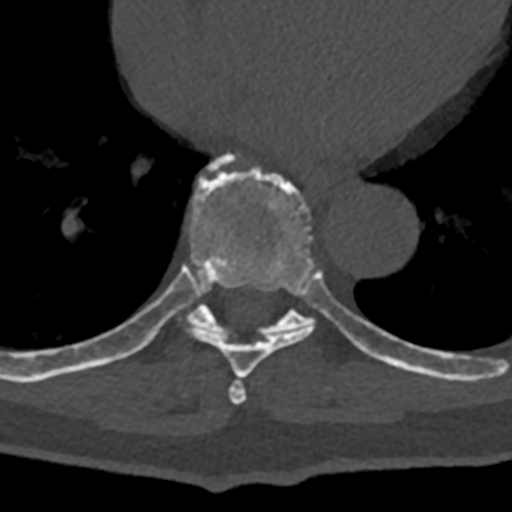
CT including the spine, one axial slice. Slice 690 of 797 in the series (ordered by position). 120 kVp. Bone window (W 1800 / L 400 HU). 512 × 512 image matrix. Patient: male, 74 years. Case-level facts recorded for this patient, not image findings: primary cancer: renal.
Structures marked on this image (semi-automatic segmentation, software-assisted and operator-edited):
- T7 vertebra: bounding box [x1, y1, x2, y2] px = [229, 377, 247, 404]
- T8 vertebra: [70, 154, 386, 378]
- T9 vertebra: [104, 265, 432, 376]